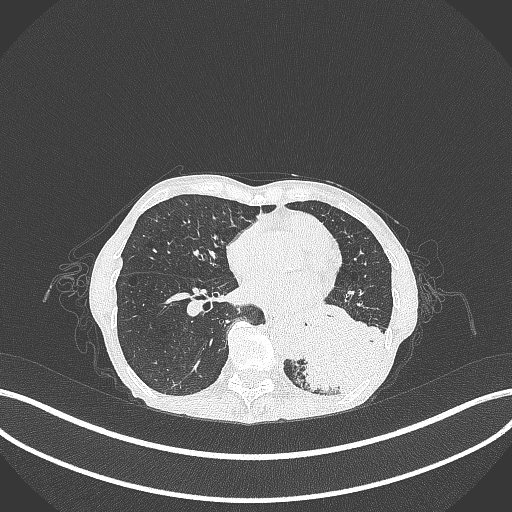
Chest CT, one axial slice; position 103 of 347 along the scan axis; reconstruction kernel B70f; lung window (W 1500 / L -600 HU); 1 mm slice thickness; 512 × 512 image matrix, field of view 400 × 400 mm. Patient: female, 70 years. Case-level facts recorded for this patient, not image findings: clinical TNM (as recorded): T3 N0 M0.
Outlined on this slice (bounding box drawn by a radiologist):
- lung tumour (recorded histology: small cell carcinoma): bounding box <292,304,384,393> (left, top, right, bottom; pixels)